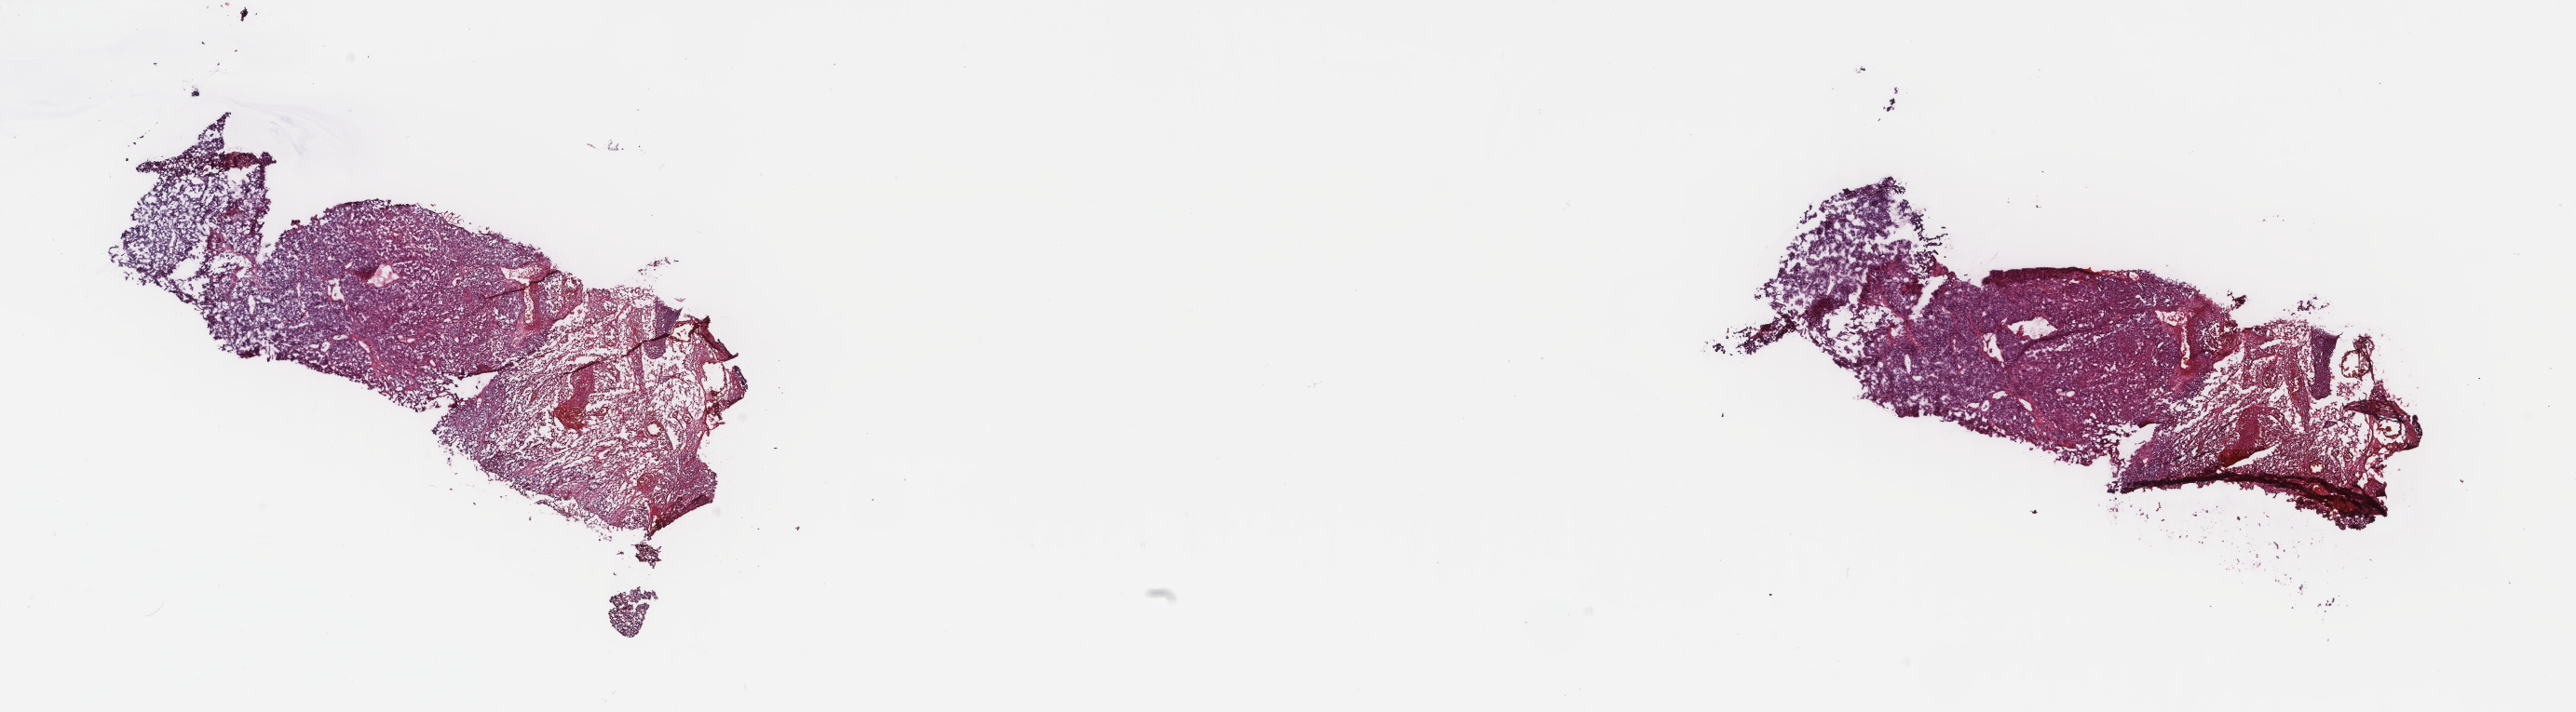
H&E whole-slide image, a low-resolution overview of the entire scanned area, about 22.0 x 6.1 mm (from a 40x scan). Frozen section from the top of the tissue portion. Primary tumour sample from the skin. Male patient; age at initial diagnosis 63 years. Pathologist review of this section (percent, as recorded): tumour cells 100%, tumour nuclei 95%.
Diagnosis: Malignant melanoma, NOS.